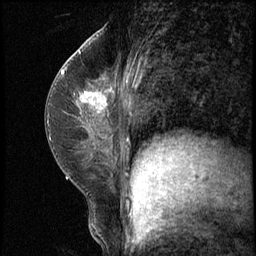
Breast MRI (dynamic contrast-enhanced), one sagittal slice. Position 30 of 62 along the scan axis. 3 images stored at this slice position (order not interpretable as contrast timing). 1.5 T. TE 4.2 ms, TR 8.7 ms. 256 × 256 image matrix. Patient: female, 35 years. From the clinical record (not read from this slice): setting: breast cancer imaged before/during neoadjuvant chemotherapy; receptor status: HER2-positive.
Annotated regions visible in this slice (semi-automatically segmented with operator editing):
- analysis volume of interest (the breast-tissue region the enhancement analysis was run in; not a lesion): box from (x=71, y=78) to (x=120, y=139) px
- tumour enhancement mask (voxels above the 140 % enhancement threshold inside the analysis volume of interest): (x=81, y=93)–(x=105, y=107)